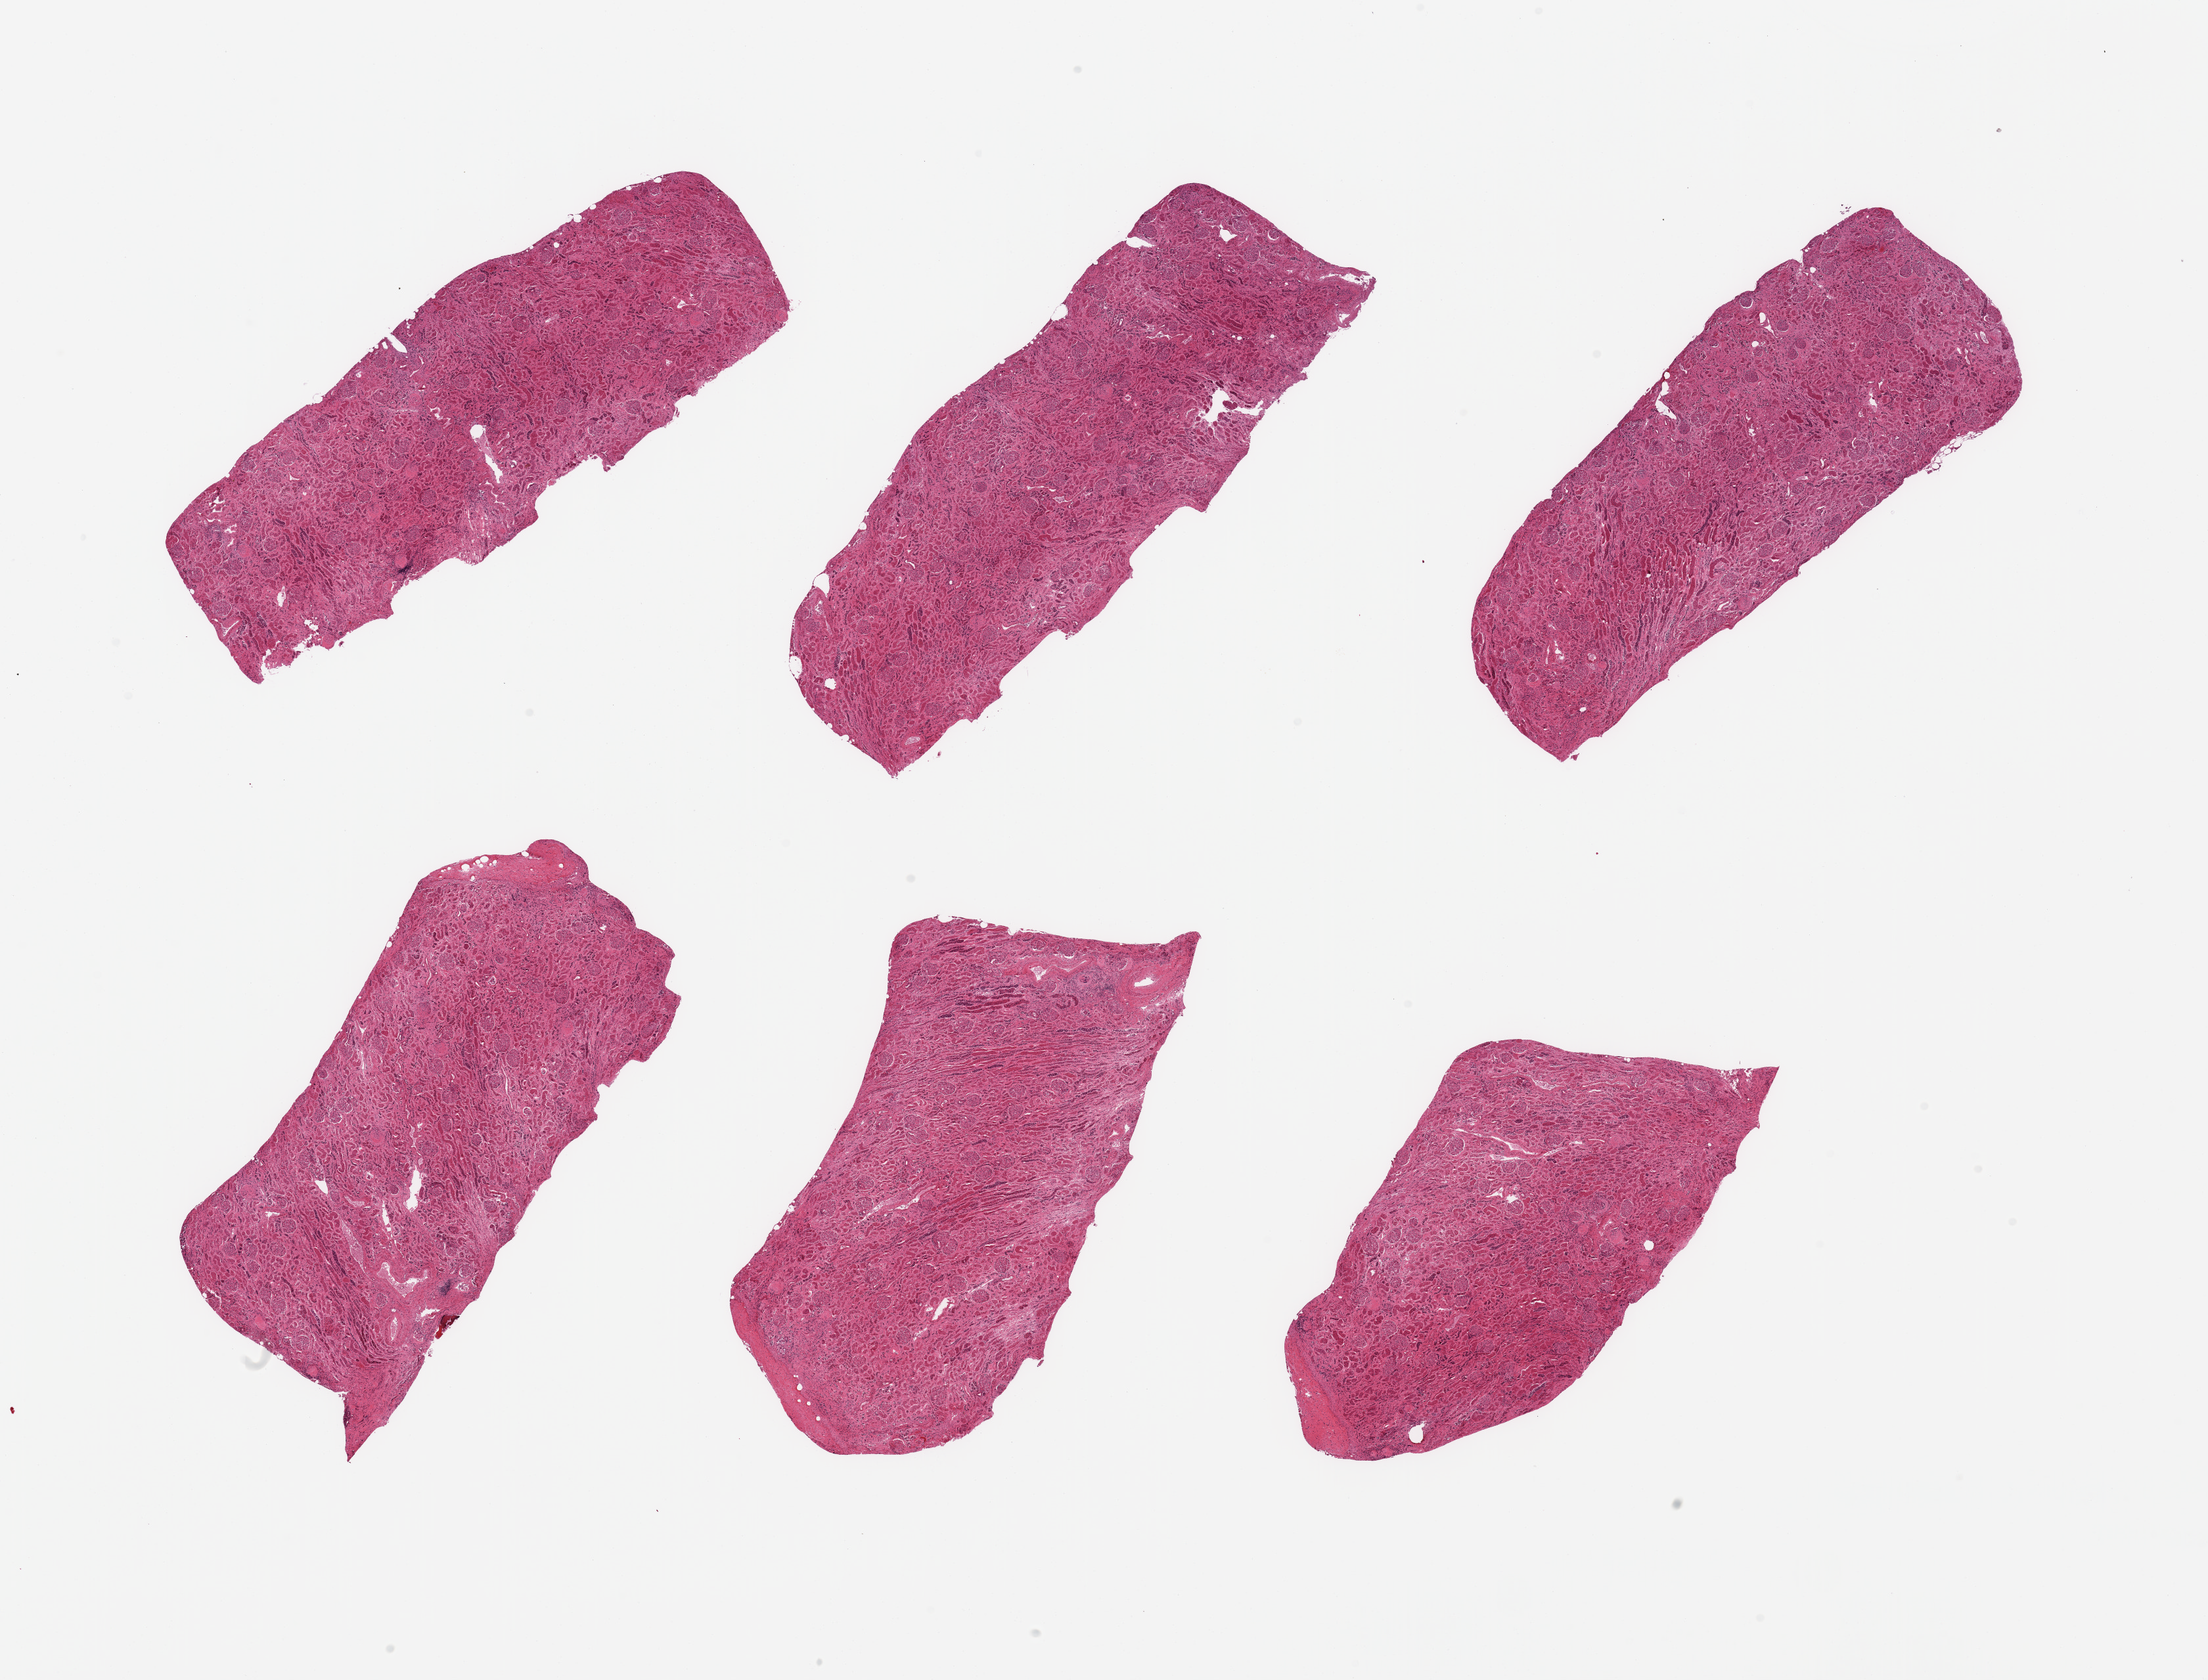
Whole-slide image, H&E stain, brightfield, whole scanned area (about 26.6 x 20.2 mm, slide scanned at 20x) shown as a low-resolution overview; PAXgene-fixed paraffin-embedded (PFPE) section; sampled site (target tissue): renal cortex; tissue donor sample. Donor sex: male.
- pathologist's review note for this sample: 6 pieces; tubules severely autolyzed, glomeruli intact; moderate number of sclerosed glomeruli